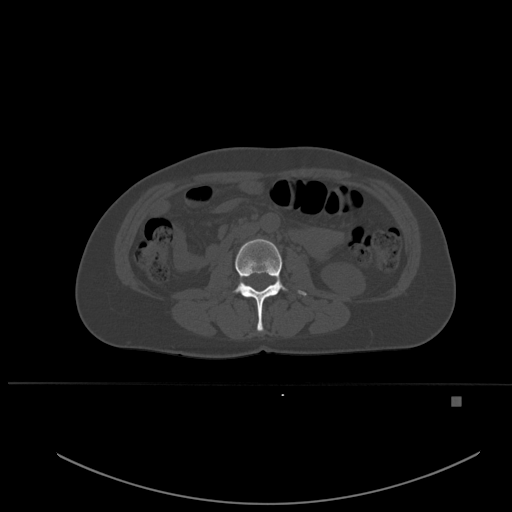
CT including the spine, one axial slice; slice 211 of 651 in the series (ordered by position); bone window (W 1800 / L 400 HU); 1.5 mm slice thickness; 512 × 512 image matrix, field of view 443 × 443 mm. Female patient, age 49 years. Case-level facts recorded for this patient, not image findings: primary cancer: breast.
Outlined on this slice (semi-automatically segmented with operator editing):
- L2 vertebra: bounding box [x1, y1, x2, y2] px = [233, 239, 307, 332]